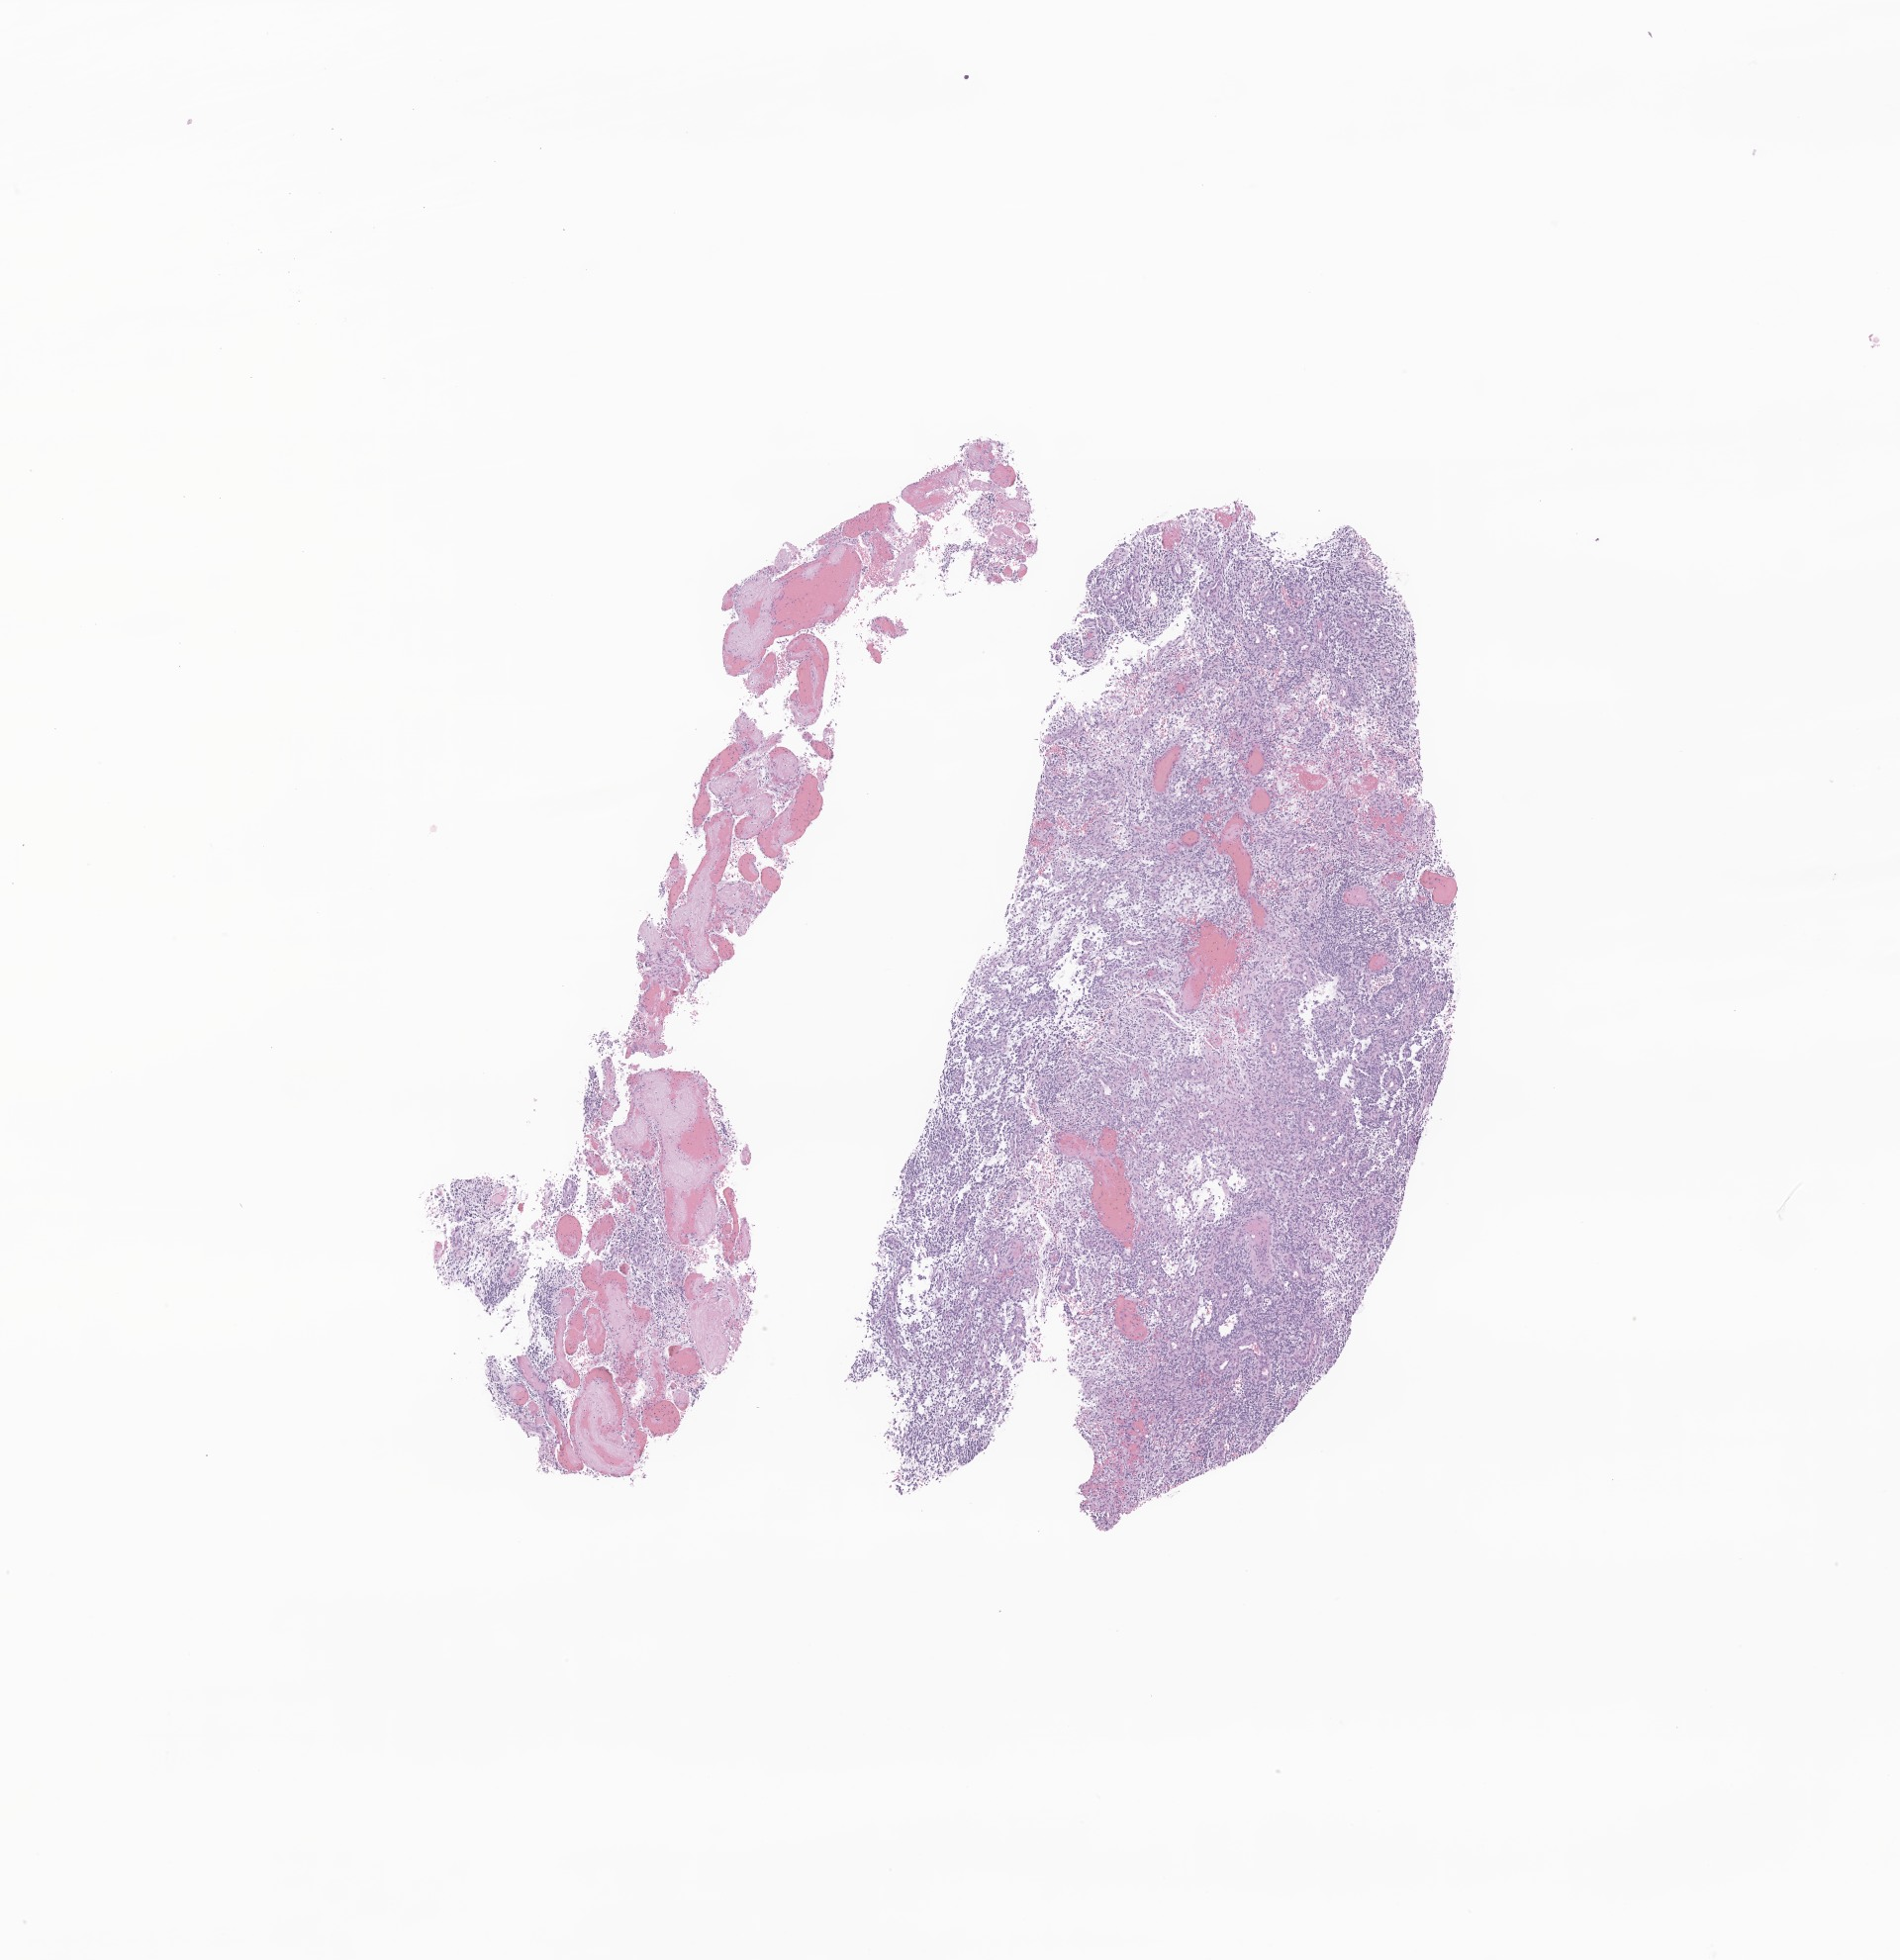
Digitized H&E-stained section of tumor tissue from the brain — whole scanned area (about 8.1 x 8.4 mm) shown as a low-resolution overview; formalin-fixed paraffin-embedded section. Patient female; age 117 months.
Diagnosis (ICD-O-3 morphology term): Glioma, malignant.